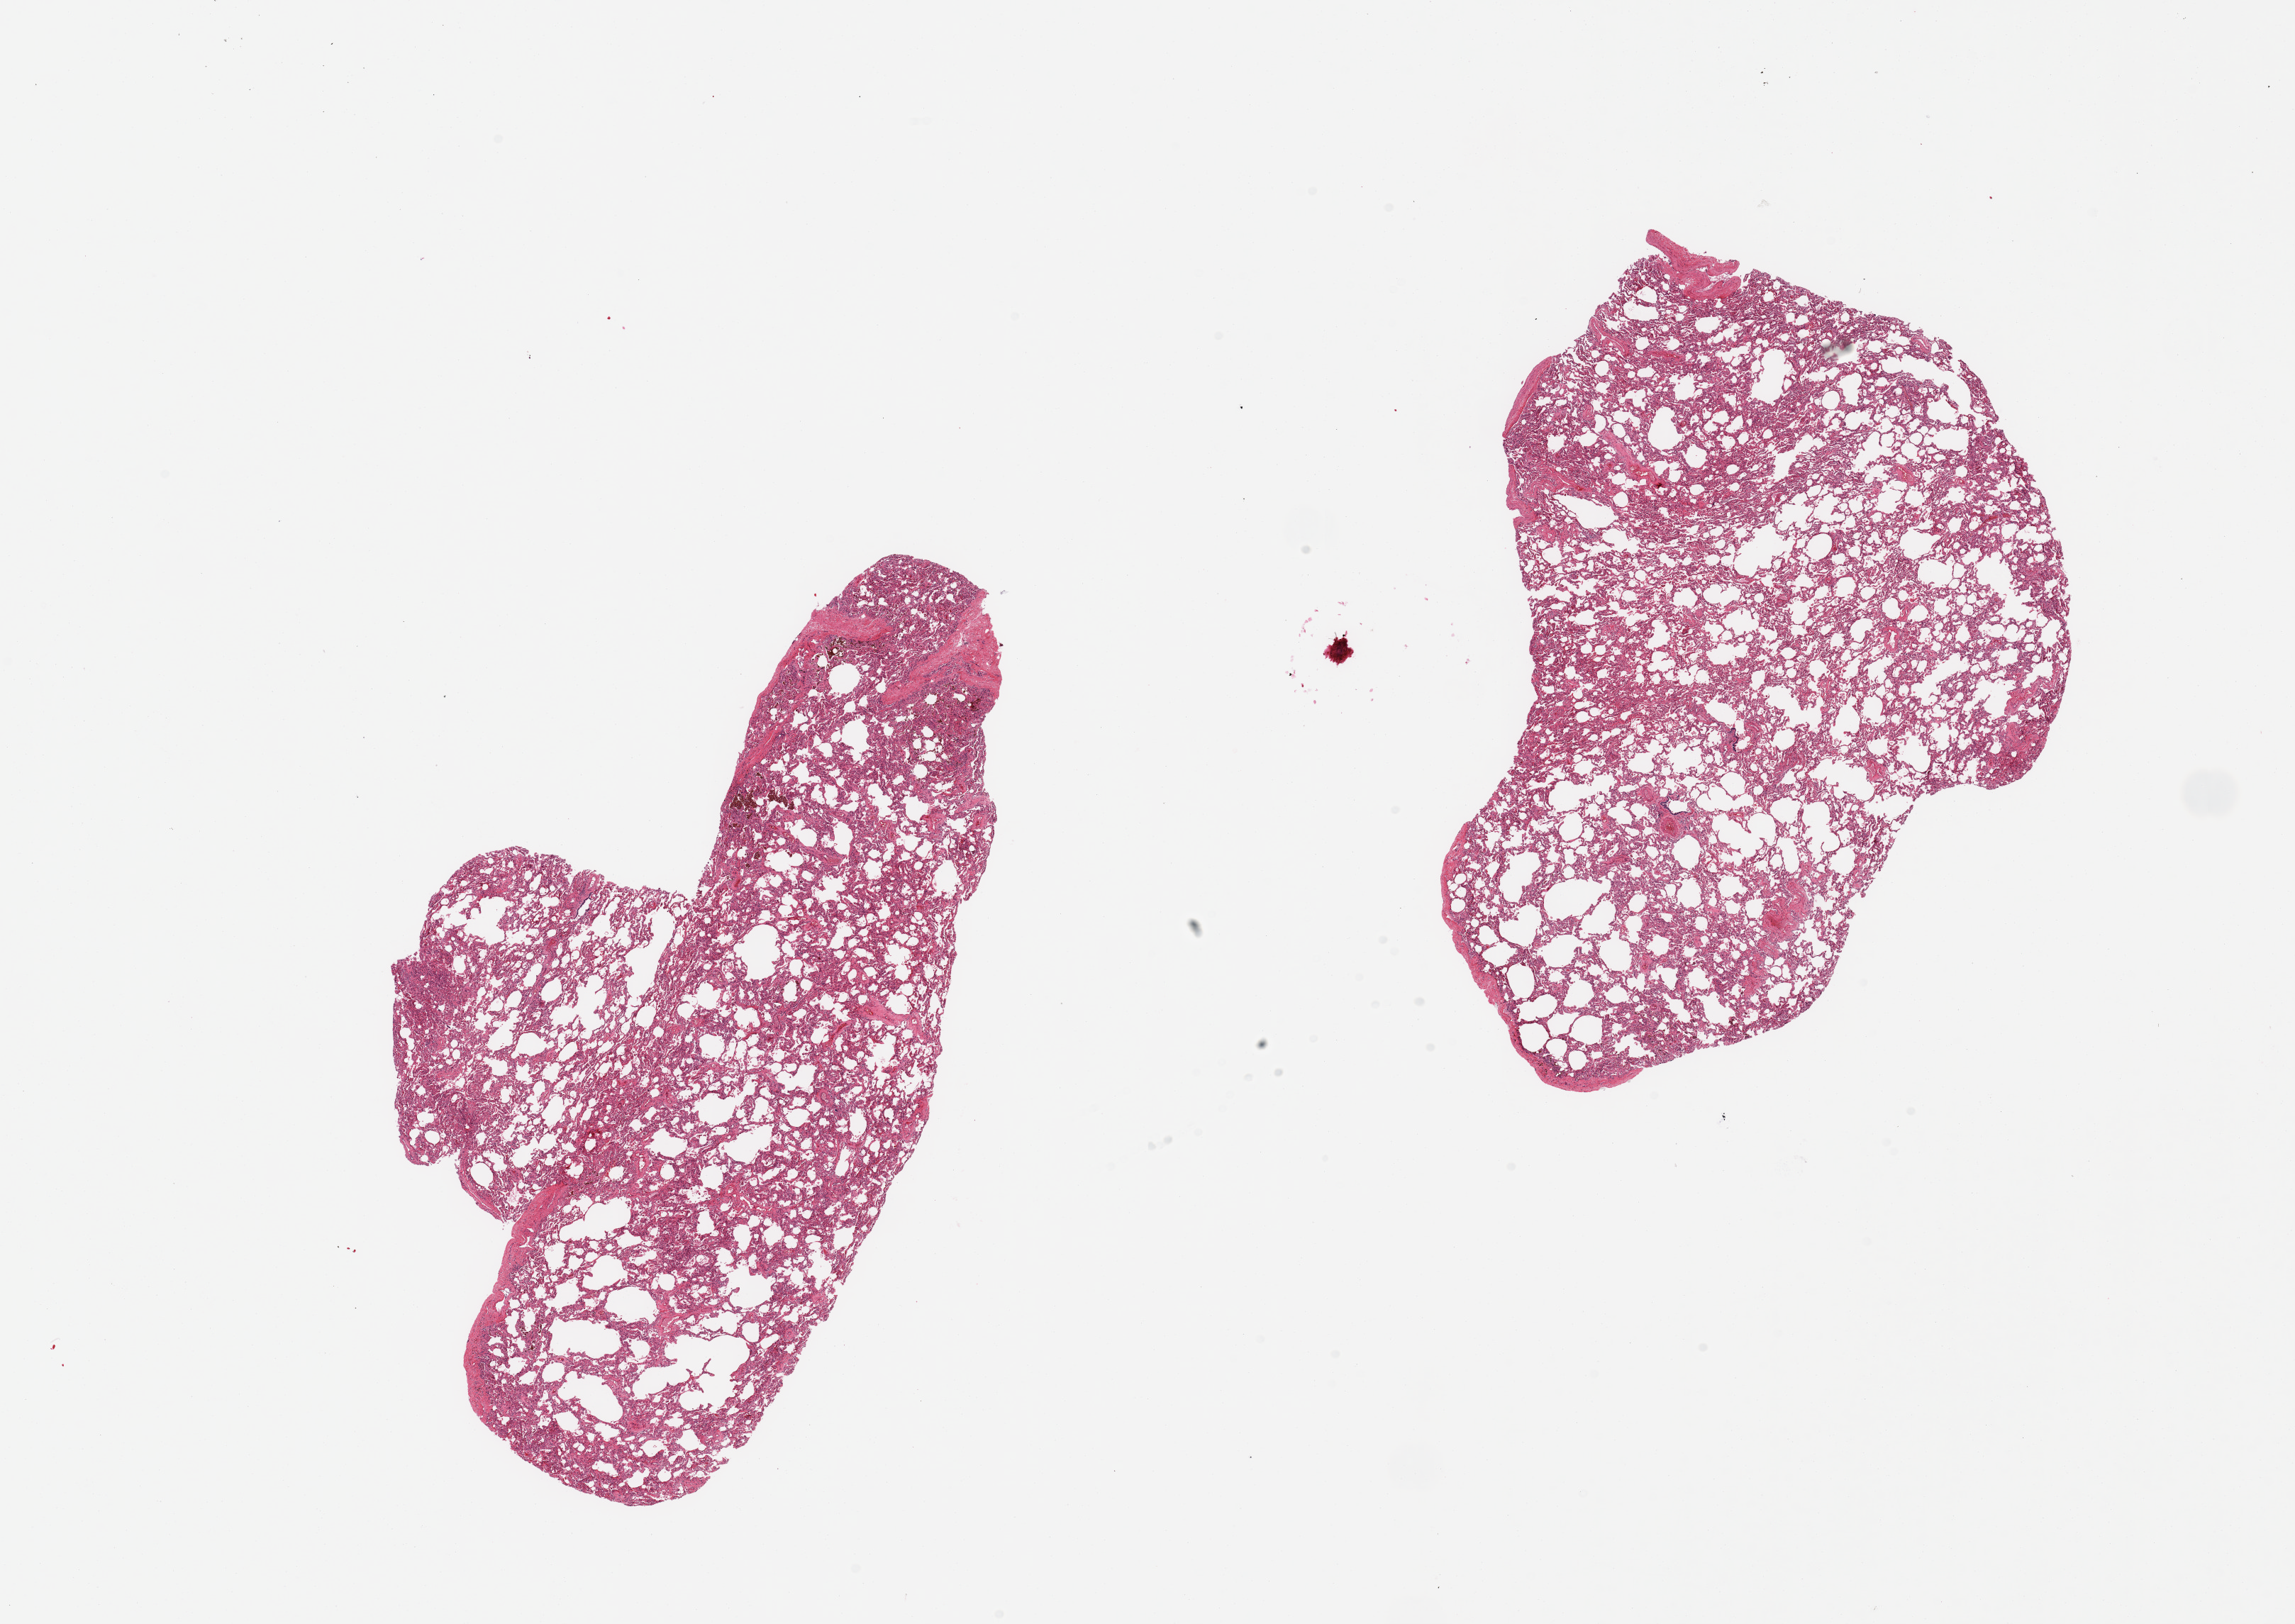
H&E whole-slide image, shown as a low-resolution overview of the whole scanned area (about 25.6 x 18.1 mm, acquisition: 20x scan), PAXgene-fixed, paraffin-embedded tissue, sampled site (target tissue): lung, donor tissue sample. Donor sex: female.
- pathologist's review note for this sample: 2 pieces; focal pigmented alveolar macrophages